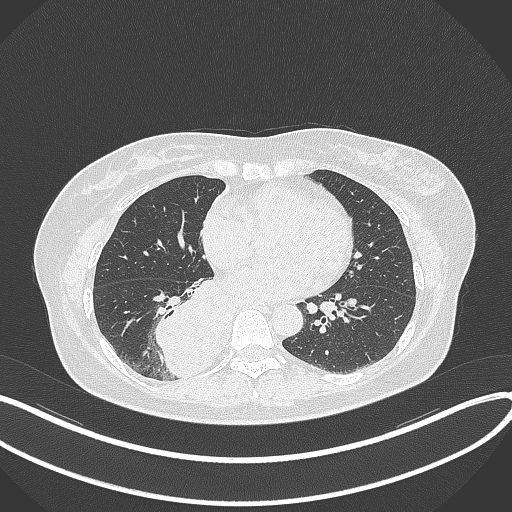
Chest CT, one axial slice; position 148 of 331 along the scan axis; reconstruction kernel B70f; 120 kVp; lung window (W 1500 / L -600 HU); 512 × 512 image matrix. Female patient, age 54 years. Case-level facts recorded for this patient, not image findings: clinical TNM (as recorded): T4 N0 M0.
Structures marked on this image (bounding box drawn by a radiologist):
- lung tumour (recorded histology: adenocarcinoma): bounding box (x1, y1, x2, y2) in pixels: (151, 279, 231, 377)